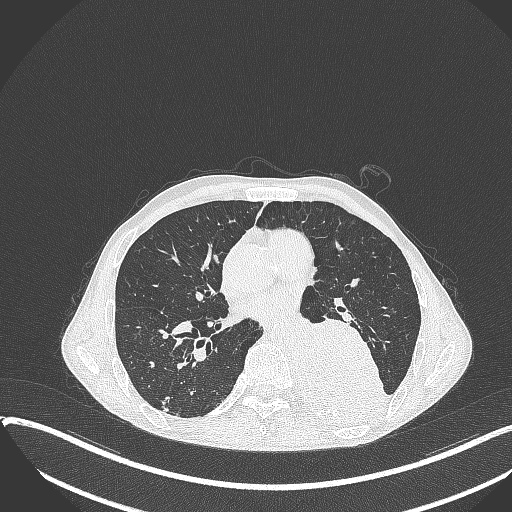
Chest CT, one axial slice. Slice 181 of 401 in the series (ordered by position). 120 kVp. Lung window (W 1500 / L -600 HU). 1 mm slice thickness. 512 × 512 image matrix, field of view 400 × 400 mm. Male patient, age 57 years. From the clinical record (not read from this slice): clinical TNM (as recorded): T4 N0 M0.
Structures marked on this image (bounding box drawn by a radiologist):
- lung tumour (recorded histology: squamous cell carcinoma): bounding box <302,313,395,427> (left, top, right, bottom; pixels)